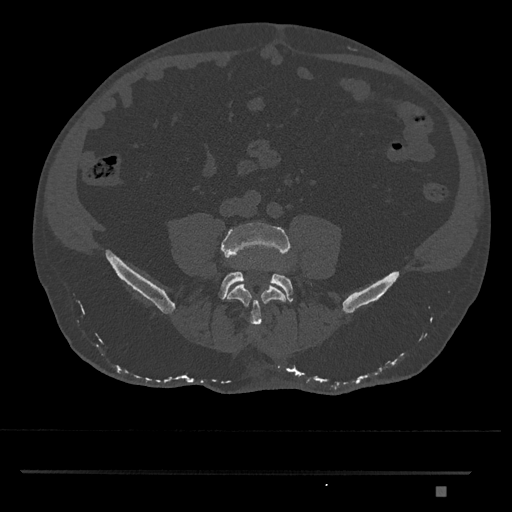
CT including the spine, one axial slice. Position 586 of 1134 along the scan axis. Reconstruction kernel Br40s/3. Bone window (W 1800 / L 400 HU). 0.5 mm slice thickness. 512 × 512 image matrix, field of view 429 × 429 mm. Patient: male, 65 years. From the clinical record (not read from this slice): primary cancer: prostate.
Outlined on this slice (semi-automatic segmentation, software-assisted and operator-edited):
- L4 vertebra: bounding box (x1, y1, x2, y2) in pixels: (220, 222, 291, 326)
- L5 vertebra: (218, 271, 294, 302)